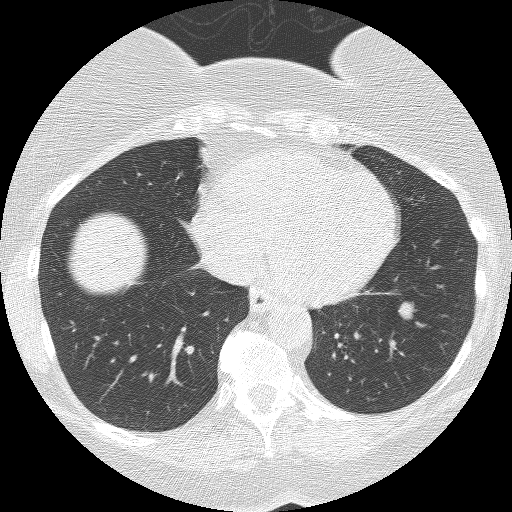
Chest CT (low-dose screening protocol), one axial image; third screening round (two years after baseline); lung window (W 1500 / L -600 HU); lung (sharp) reconstruction kernel (BONE); 512 × 512 image matrix. Female participant, aged 55 years at enrolment. Former smoker at enrolment.
• Expert-annotated lung lesion, bounding box [x1, y1, x2, y2] px = [379, 291, 429, 337].
• The screening reader recorded 3 non-calcified nodules or masses ≥4 mm on this exam (right lower lobe, right lower lobe, left lower lobe); which of them this box marks is not recorded.
• Official screen result: positive, no significant change: stable abnormalities potentially related to lung cancer, unchanged since the prior screening exam.
• Later outcome: lung cancer diagnosed 356 days after this screen — carcinoid tumor, NOS, left lower lobe, carcinoid, stage not assessed, 10 mm at pathology.